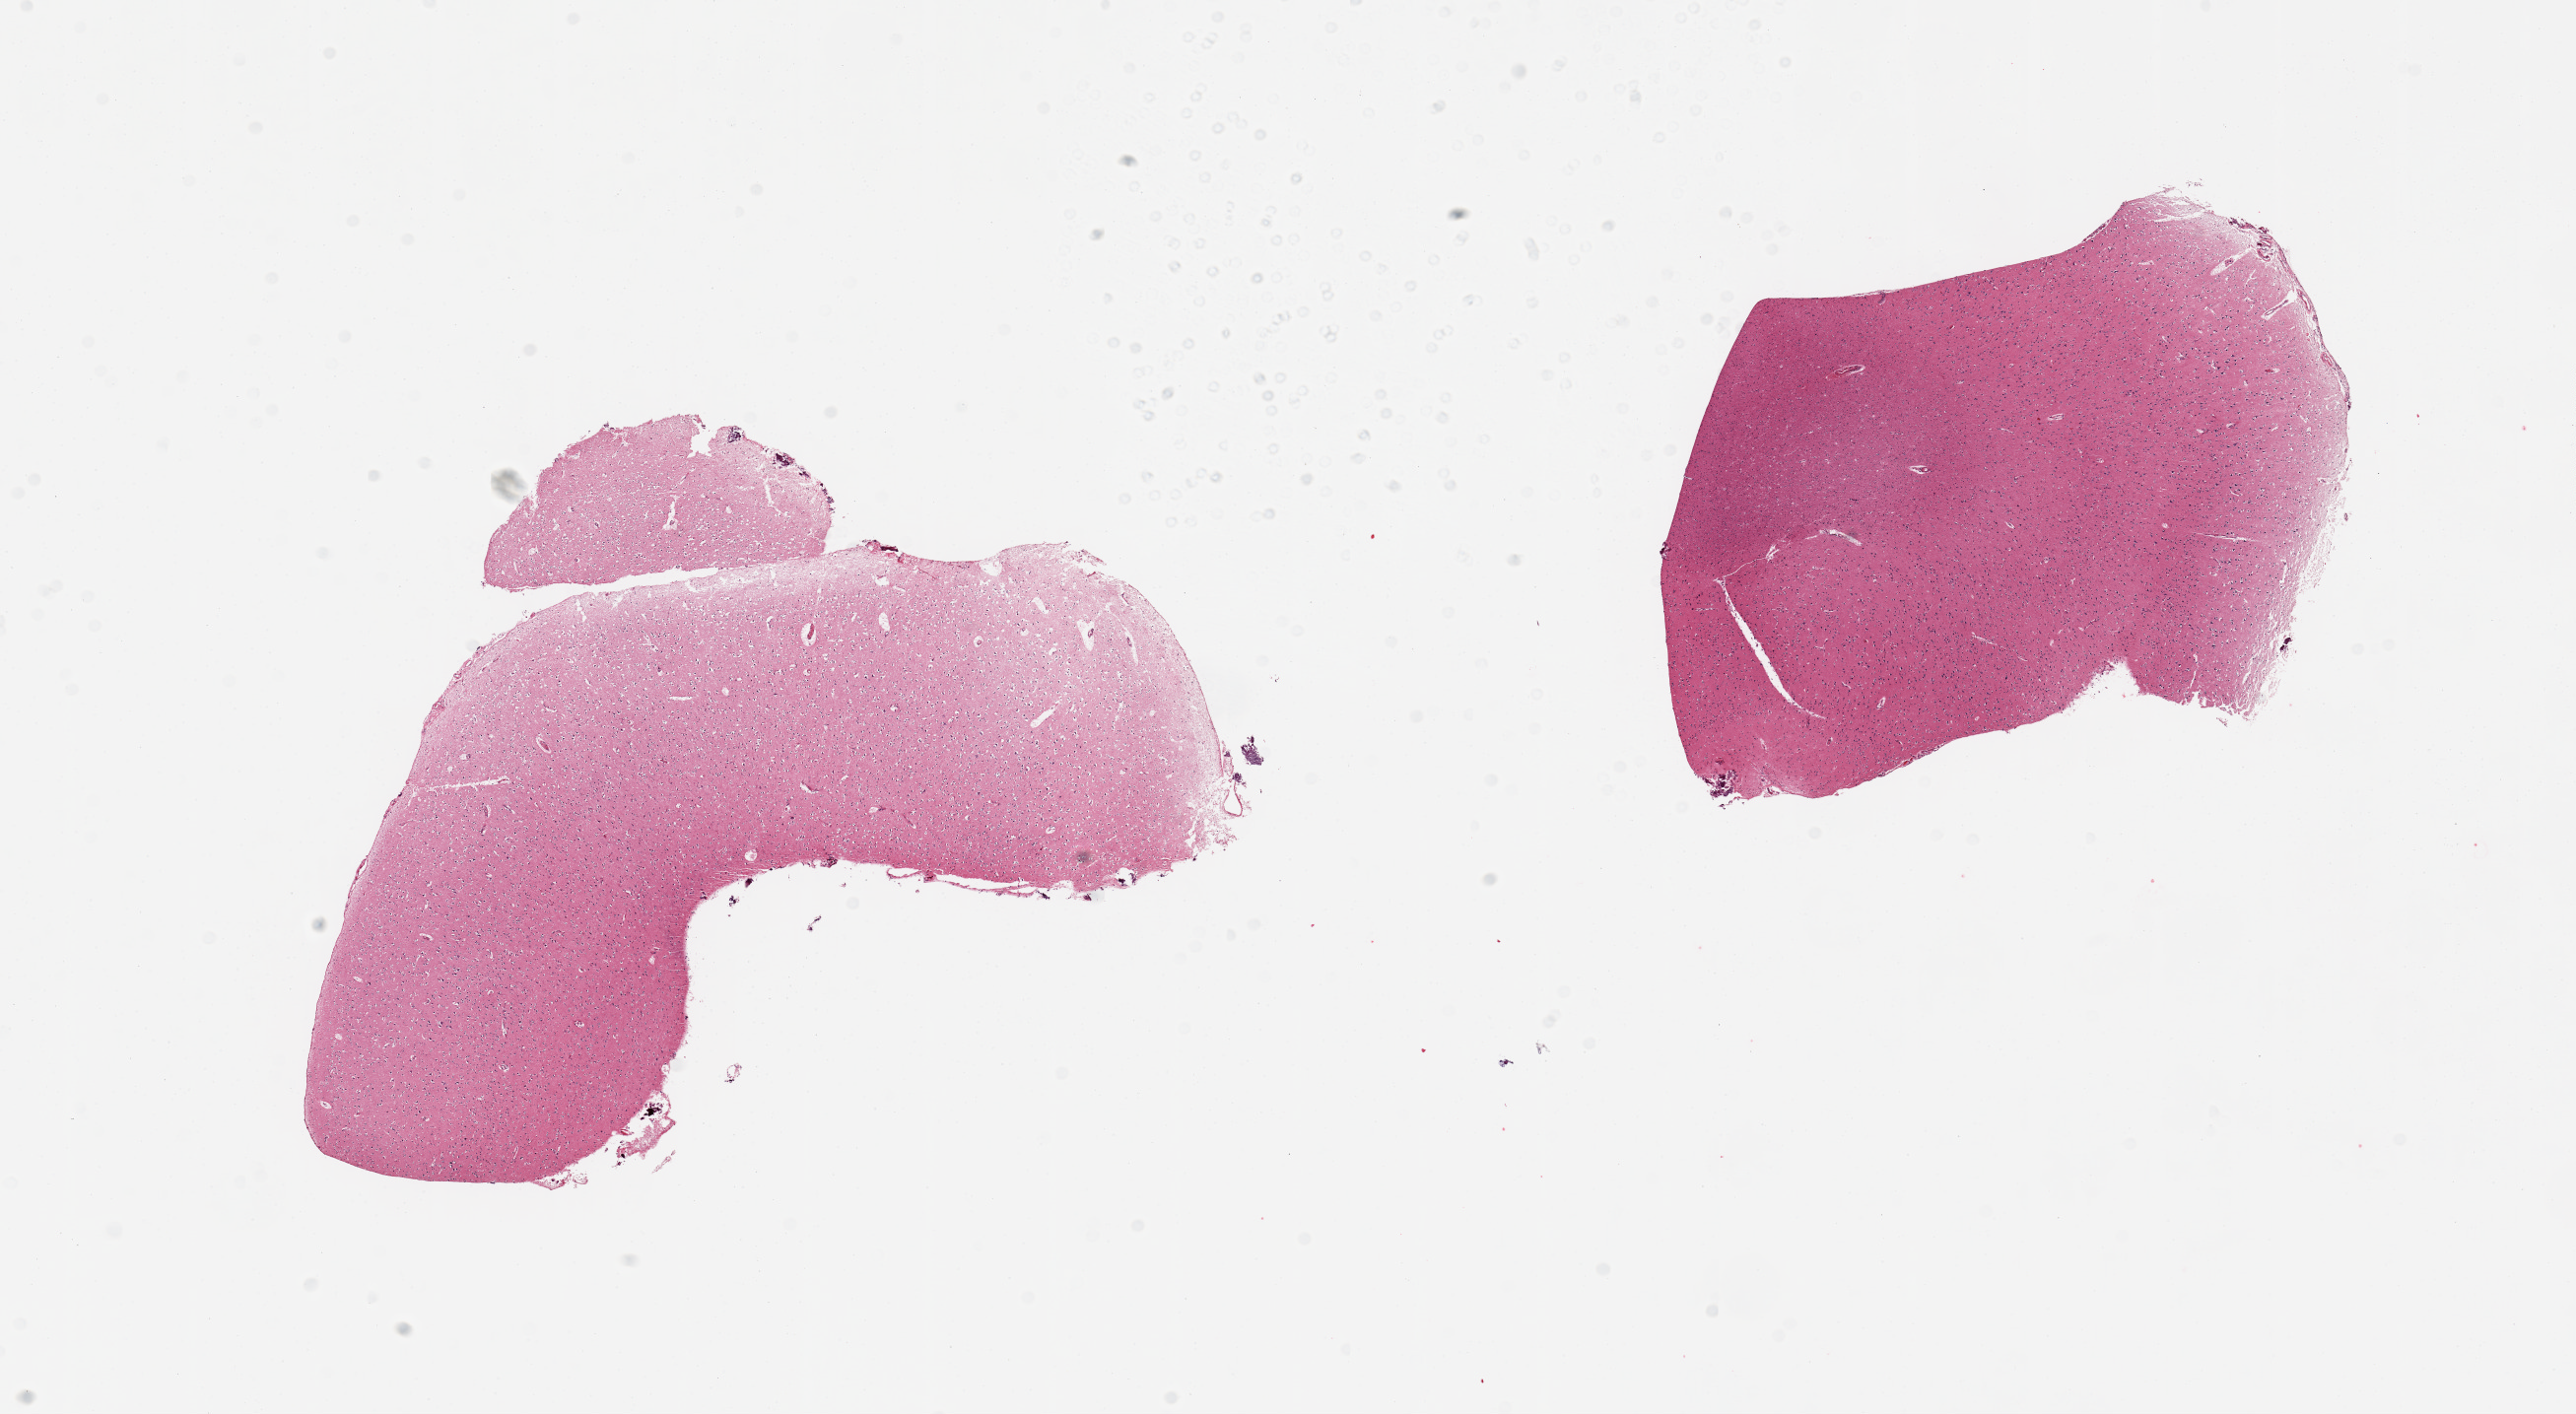
H&E whole-slide image — low-resolution overview of the scanned area, about 20.7 x 11.3 mm. PAXgene-fixed paraffin-embedded (PFPE) section. Target tissue: cerebral cortex. Donor tissue sample. Donor: male.
Review note (as recorded): 2 pieces, no abnormalities.